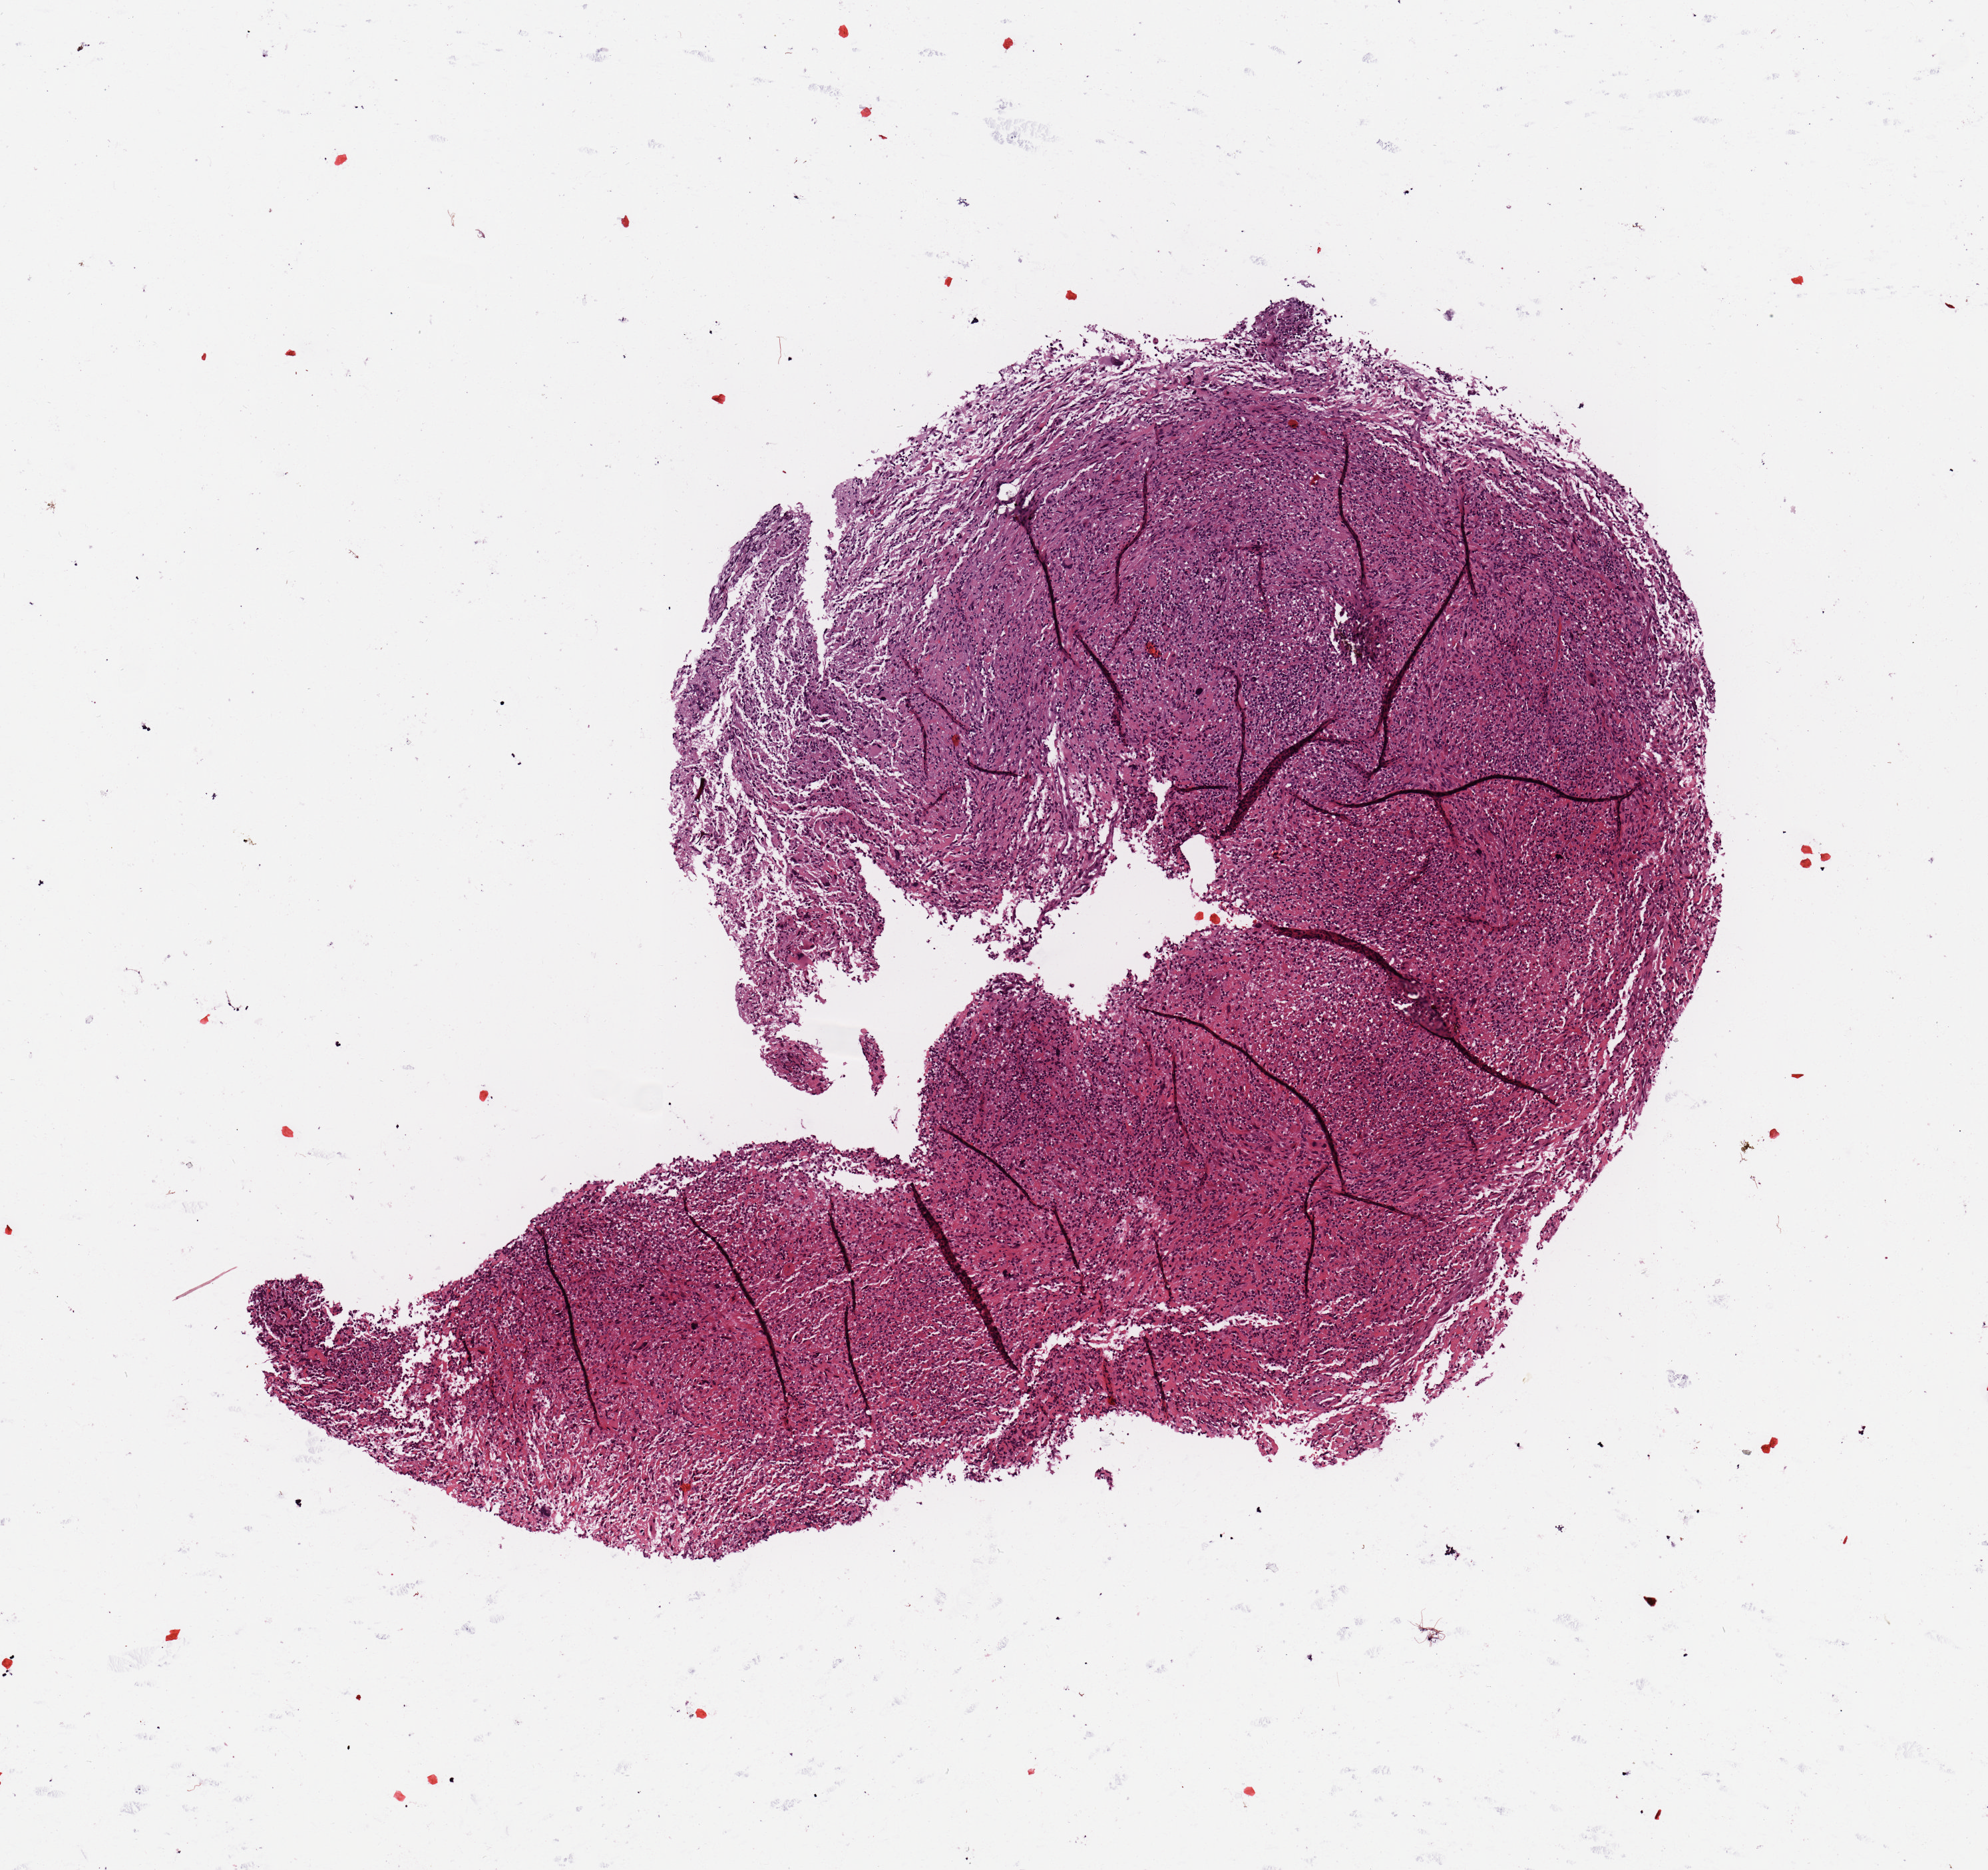
Digitized H&E-stained tissue section (whole slide) — whole scanned area (about 5.9 x 5.6 mm) shown as a low-resolution overview, tumour tissue sample, sampled site: brain. Patient: female, age 63 years. Pathologist review of this section (percent, as recorded): tumour nuclei 85%, necrosis 2%.
- primary tumour site (as recorded): temporal lobe
- diagnosis: Glioblastoma